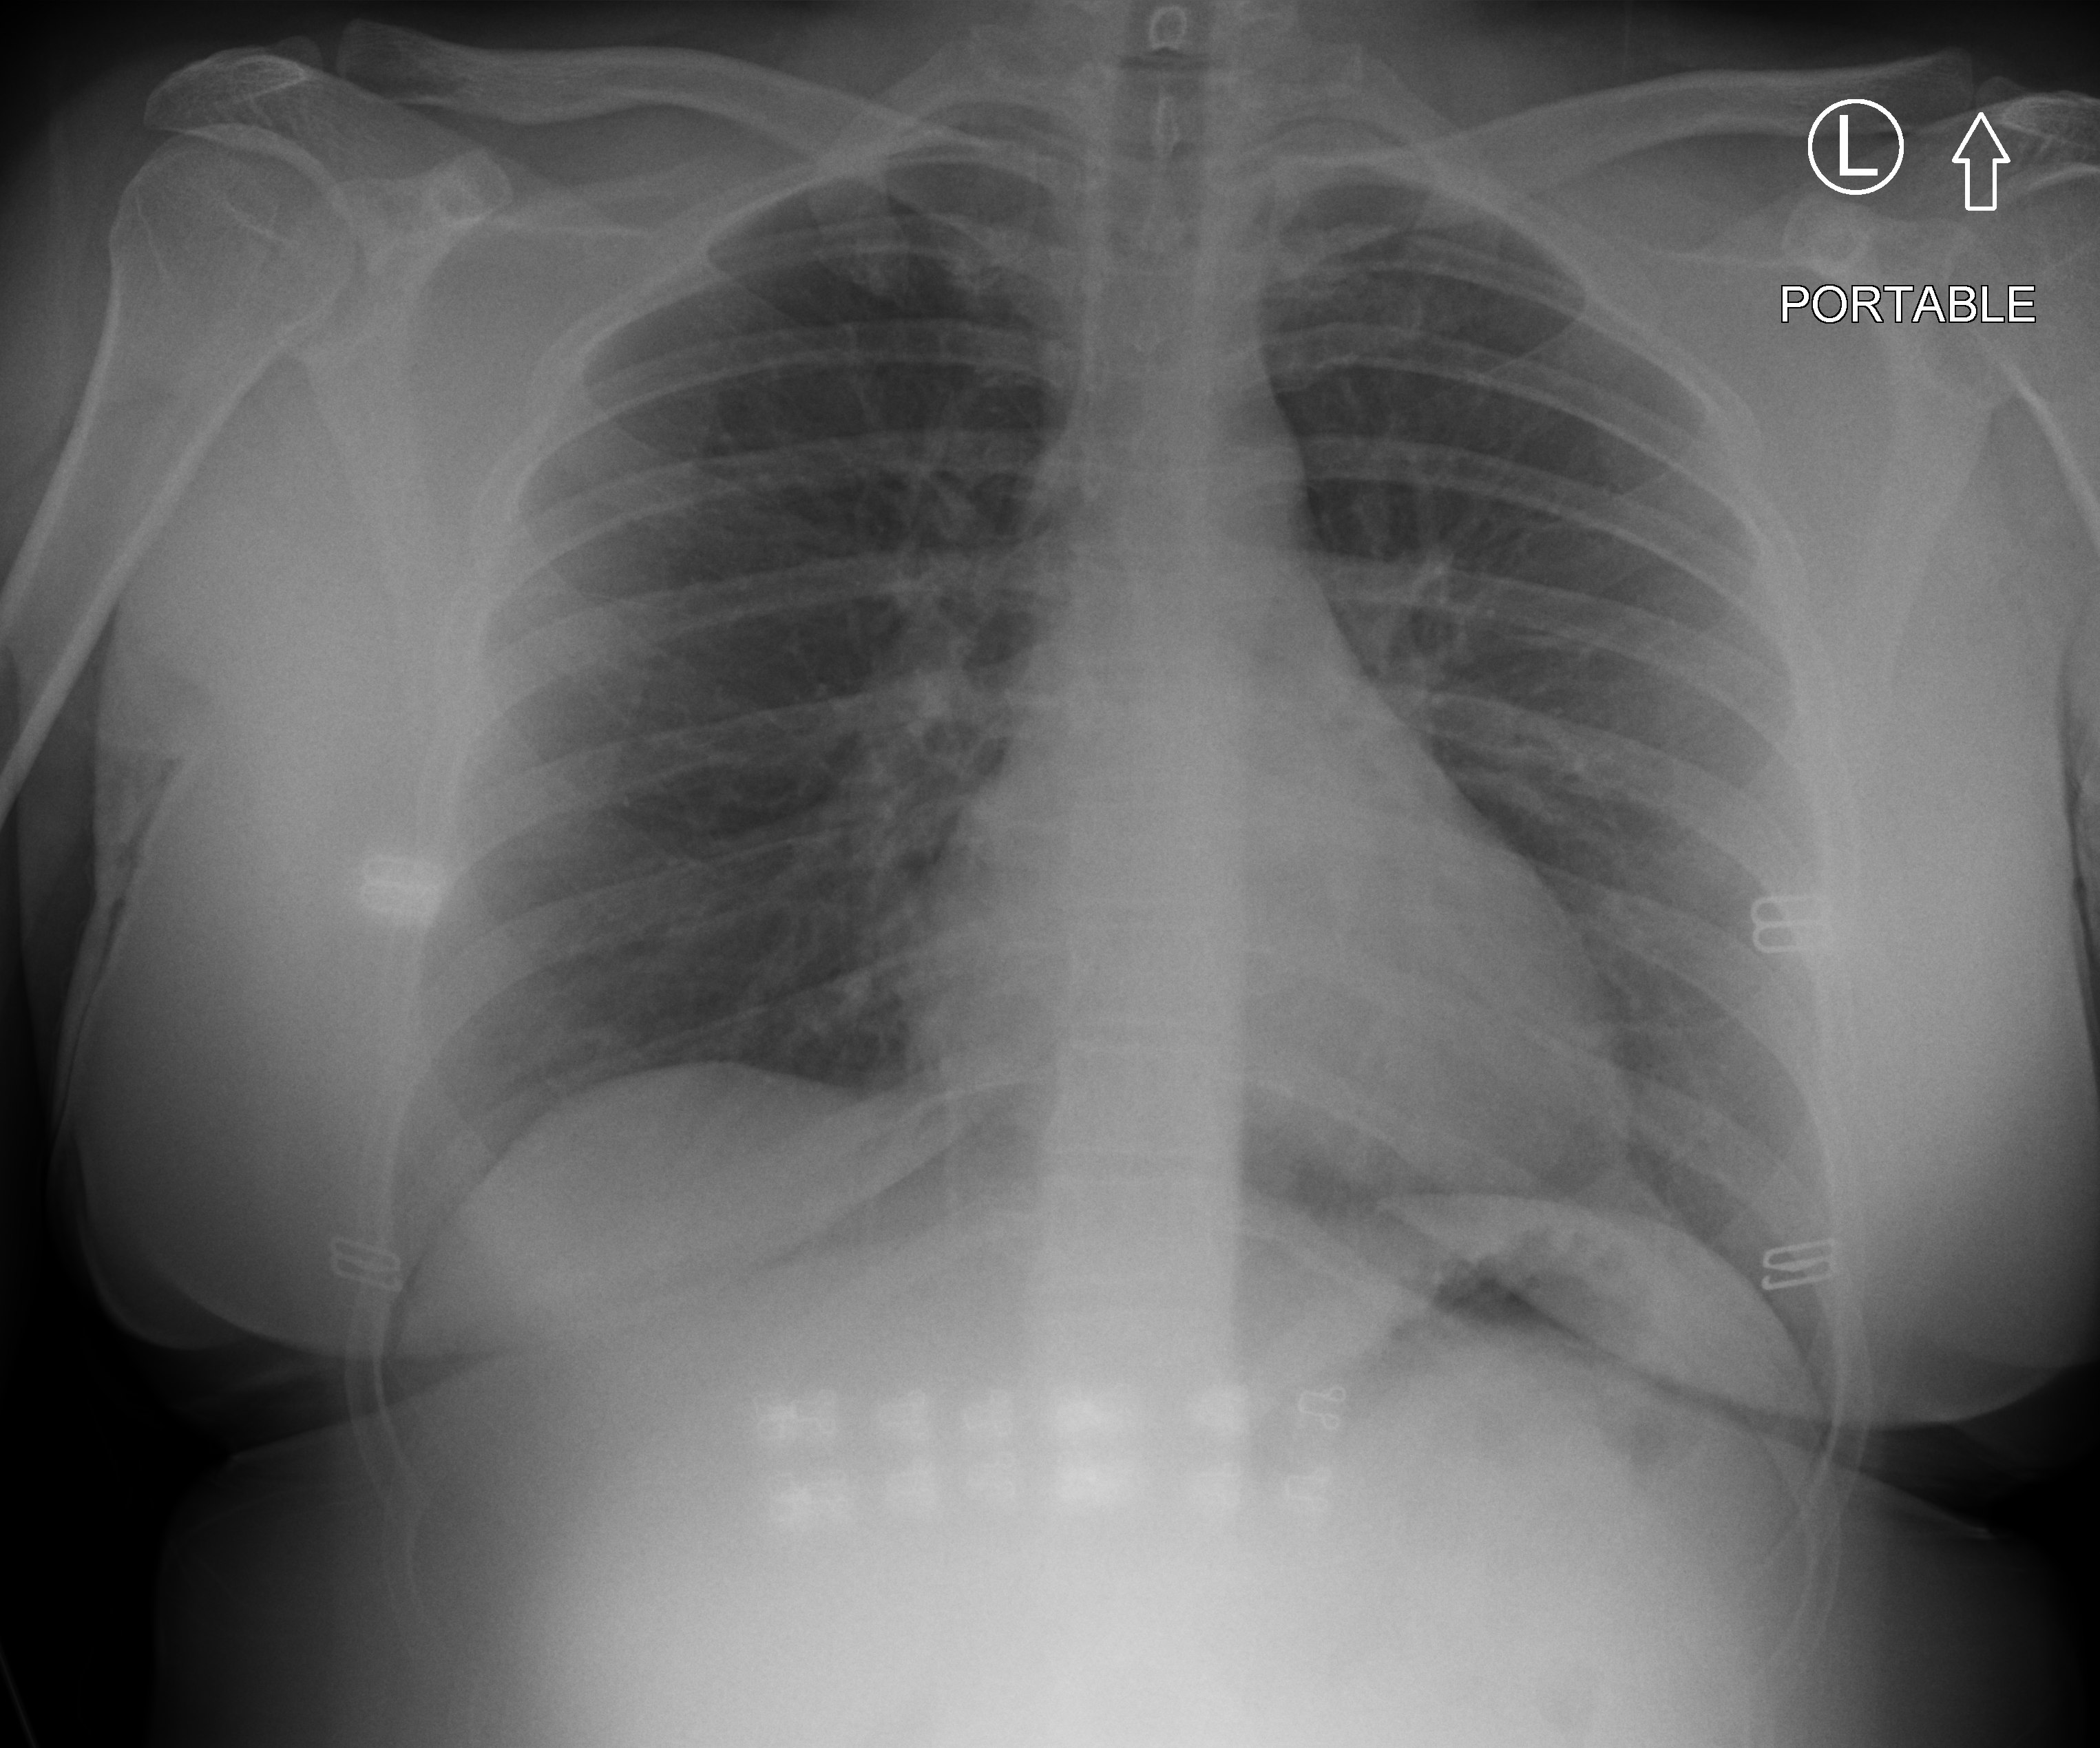
Bedside chest radiograph (computed radiography). Female patient hospitalised with COVID-19, age 18–59 years.
Hospital-stay facts (about this admission, not read from this image; timing relative to this image not recorded): mechanically ventilated during this hospital stay: no; admitted to intensive care during this hospital stay: no.